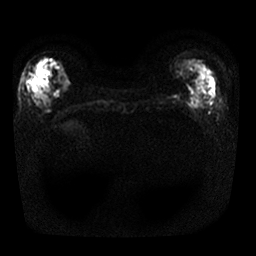
Breast MRI, one axial slice; slice 8 of 25 in the series (ordered by position); diffusion-weighted series; image 2 of 4 stored at this slice position (different b-values; order by instance number); 1.5 T; 4 mm slice thickness; 256 × 256 image matrix. Female patient.
Structures marked on this image (outlined manually by an expert reader):
- tumour on diffusion-weighted imaging: bounding box (x1, y1, x2, y2) in pixels: (36, 68, 45, 79)